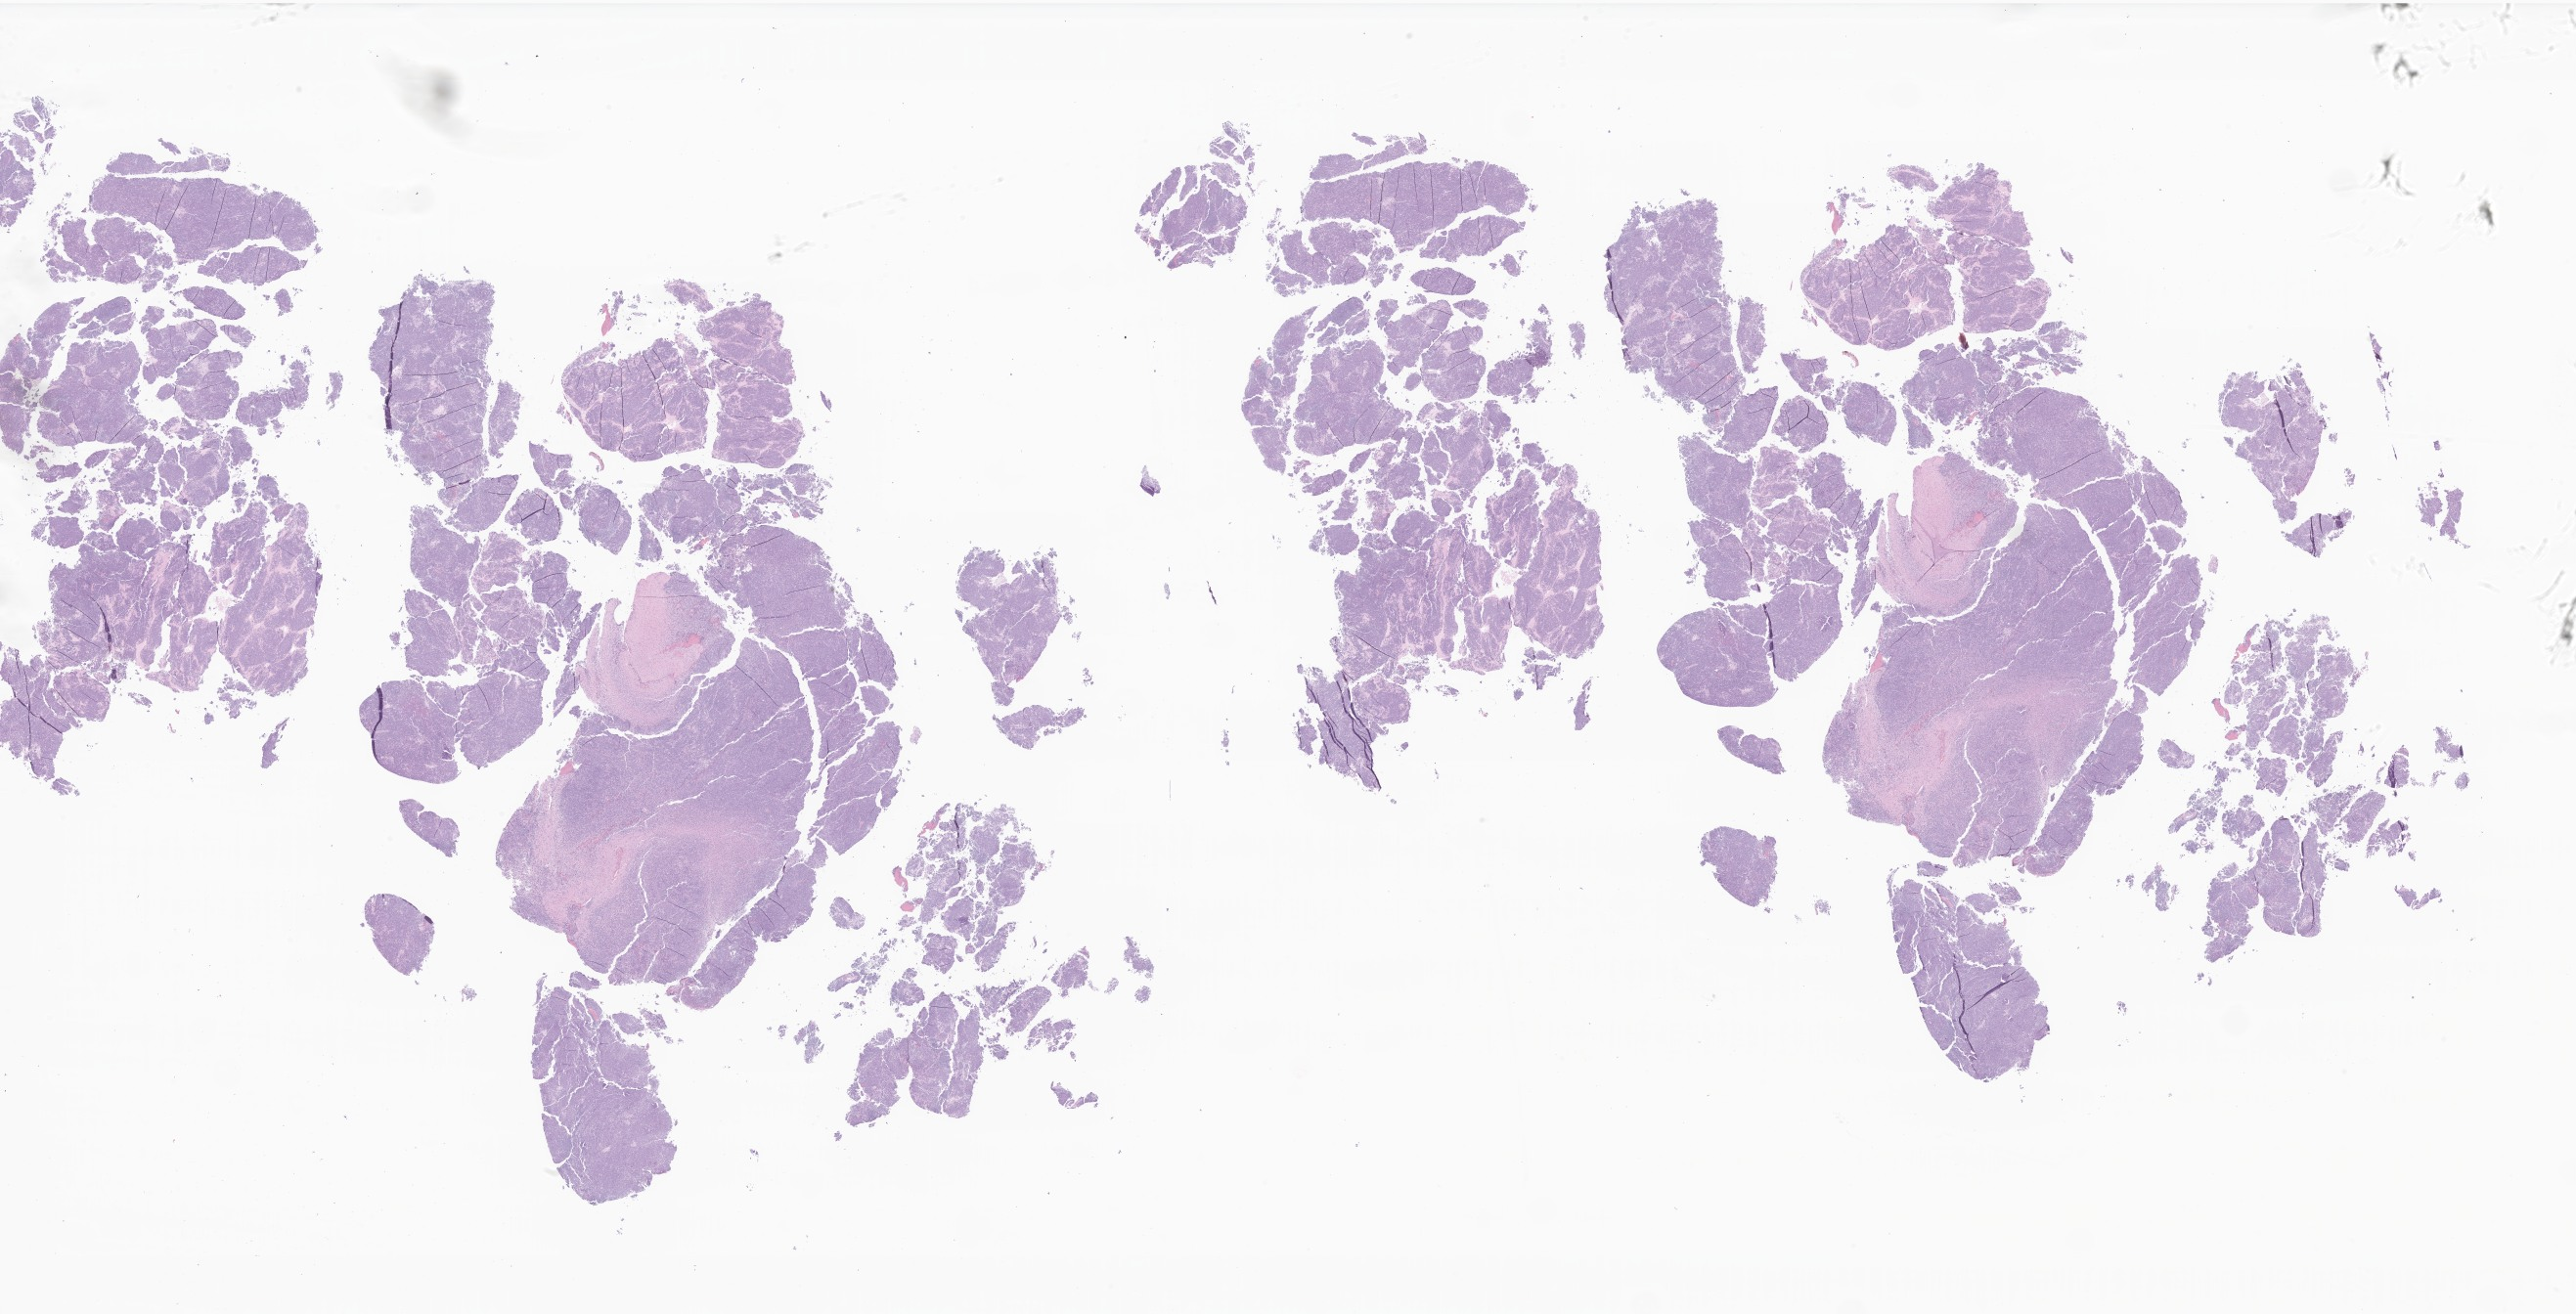
Haematoxylin and eosin whole-slide image of tumor tissue from the brain, whole scanned area (about 44.4 x 22.7 mm) shown as a low-resolution overview; formalin-fixed, paraffin-embedded (FFPE) tissue. Female patient, age 170 months.
- recorded diagnosis: Medulloblastoma, NOS